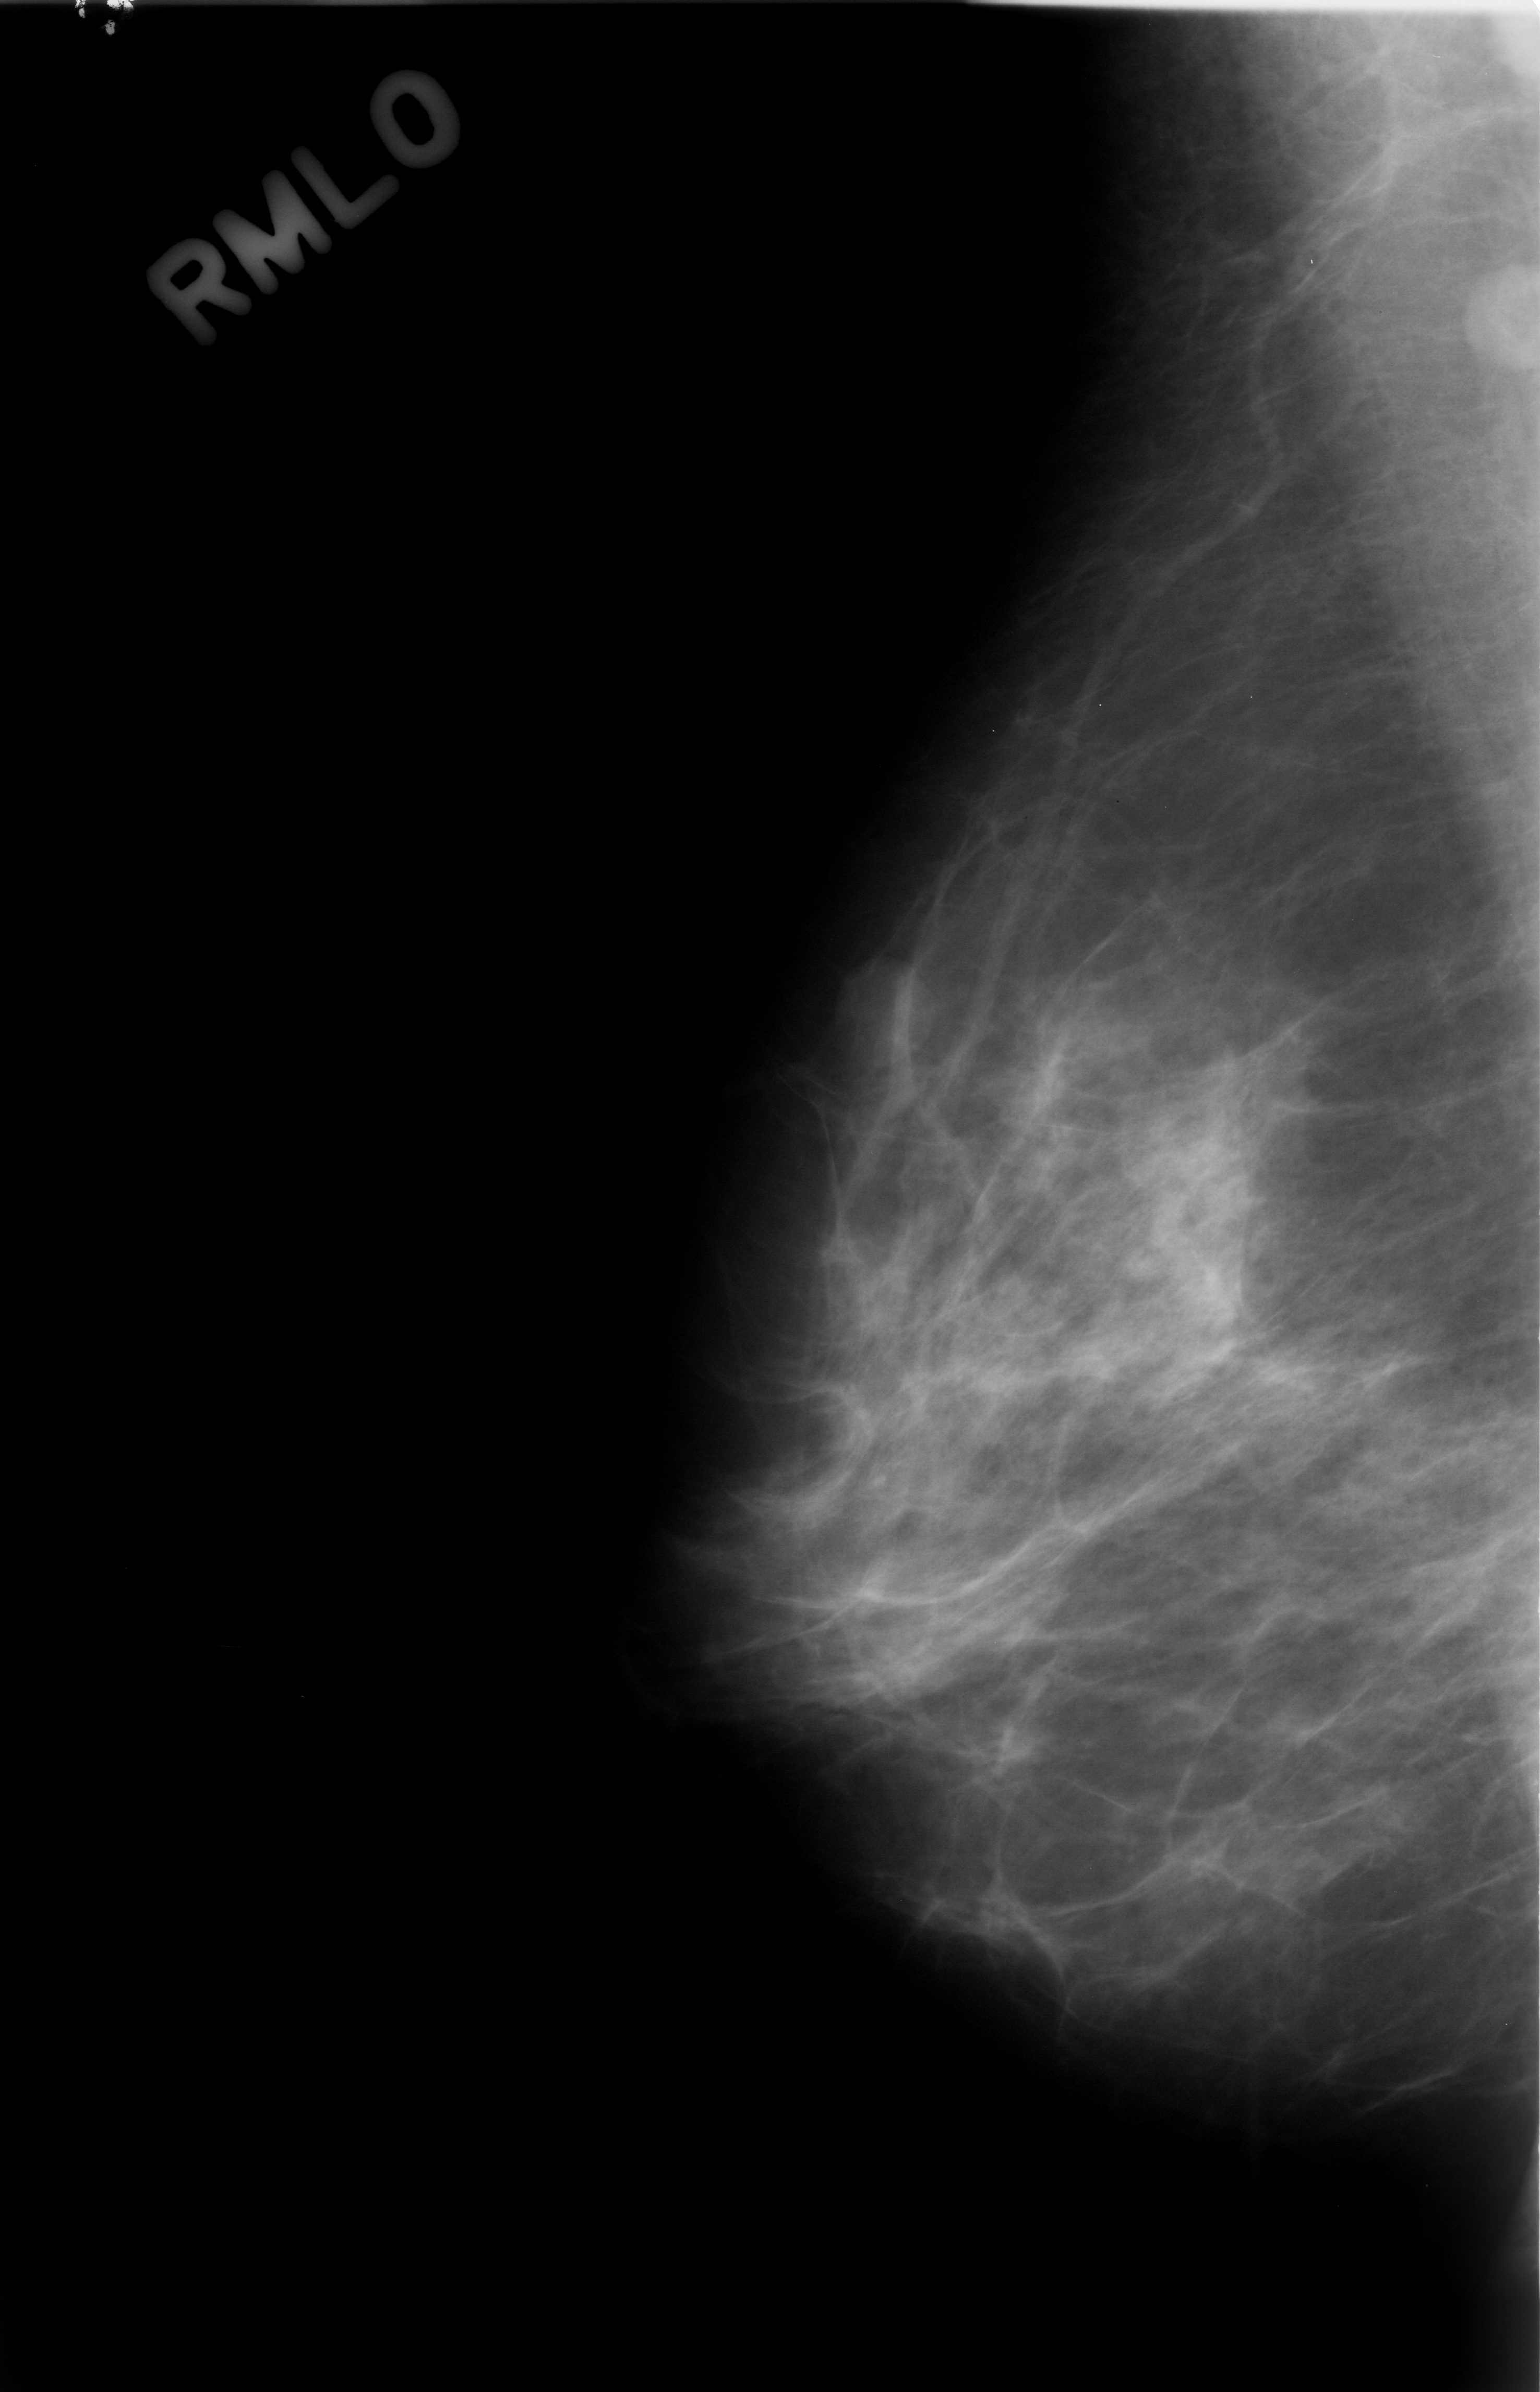
Scanned film-screen mammogram; right breast; mediolateral oblique (MLO) view; 1540 × 2392 image matrix.
Expert-marked regions of interest on this image (one box per marked abnormality):
- mass, shape round, margins circumscribed; BI-RADS assessment category 3; subtlety rating 3 on a 1 (subtle) to 5 (obvious) scale; outcome (as recorded, no biopsy): benign without callback (not worked up further): bounding box <832,946,961,1112> (left, top, right, bottom; pixels)